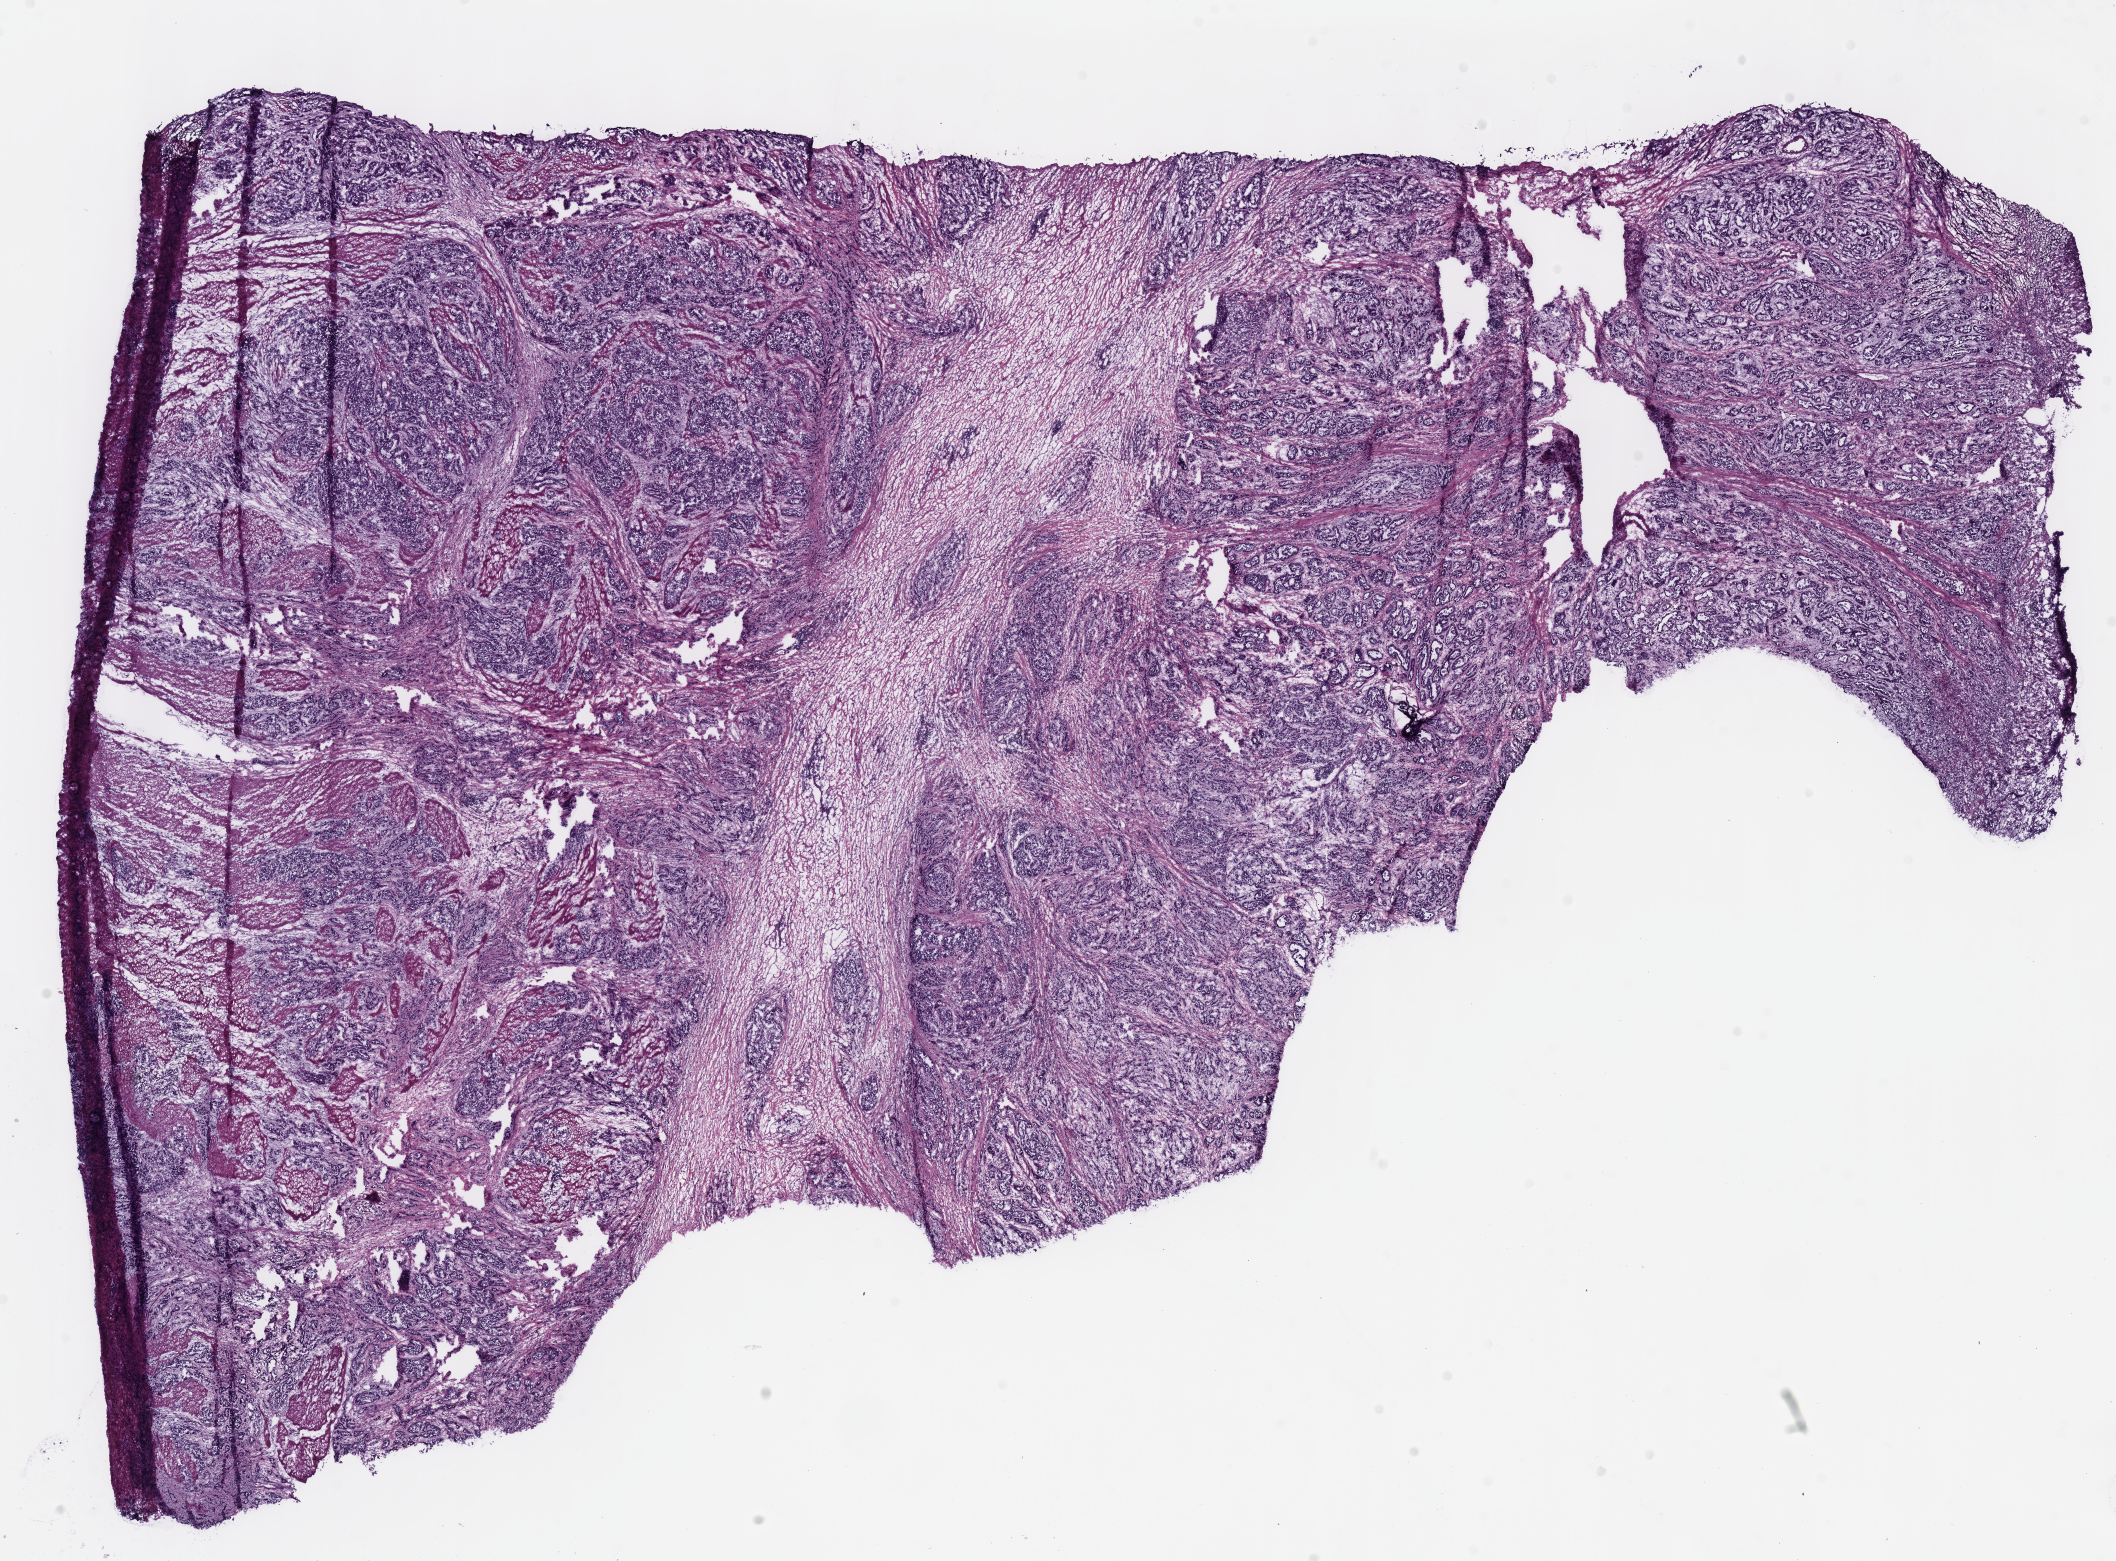
Digitized H&E-stained tissue section (whole slide), low-resolution overview of the scanned area, about 16.6 x 12.3 mm (slide scanned at 40x), frozen section from the bottom of the tissue portion, stomach, primary tumour sample. Patient: male, age at initial diagnosis 57 years. Pathologist review of this section (percent, as recorded): tumour cells 85%, tumour nuclei 85%.
Diagnosis: Adenocarcinoma, intestinal type (body of stomach).